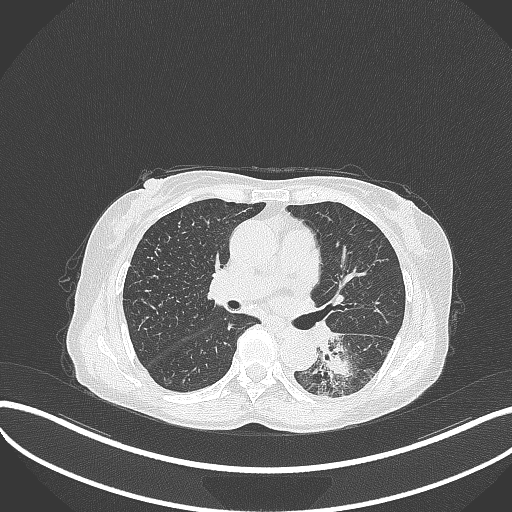
Chest CT, one axial slice; slice 176 of 370 in the series (ordered by position); reconstruction kernel B70f; lung window (W 1500 / L -600 HU); 1 mm slice thickness; 512 × 512 image matrix, field of view 400 × 400 mm. Patient: female, 78 years. From the clinical record (not read from this slice): clinical TNM (as recorded): T3 N0 M1.
Structures marked on this image (rectangle marked by the reading radiologist):
- lung tumour (recorded histology: squamous cell carcinoma): bounding box (x1, y1, x2, y2) in pixels: (312, 328, 361, 393)